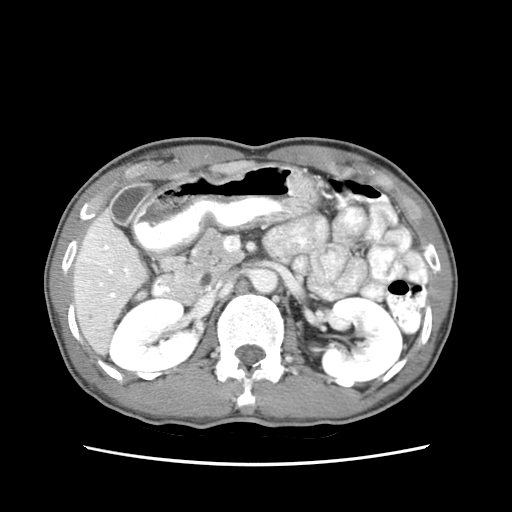
Contrast-enhanced abdominal CT (liver protocol), one axial slice; position 27 of 79 along the scan axis; soft-tissue window (W 400 / L 40 HU); 512 × 512 image matrix, field of view 320 × 320 mm. Case-level facts recorded for this patient, not image findings: diagnosis: hepatocellular carcinoma (patient treated with transarterial chemoembolisation; whether this scan precedes or follows treatment is not stated here); TNM stage (as recorded): Stage-IIIB; Child-Pugh class: A; tumour differentiation: moderately differentiated; tumour nodularity: multinodular.
Annotated regions visible in this slice (semi-automatically segmented with operator editing):
- liver parenchyma outside the tumour (the mass and vessels are separate outlines, so this box may not span the whole liver): bounding box [x1, y1, x2, y2] px = [72, 208, 146, 352]
- liver vessels: [81, 225, 132, 297]